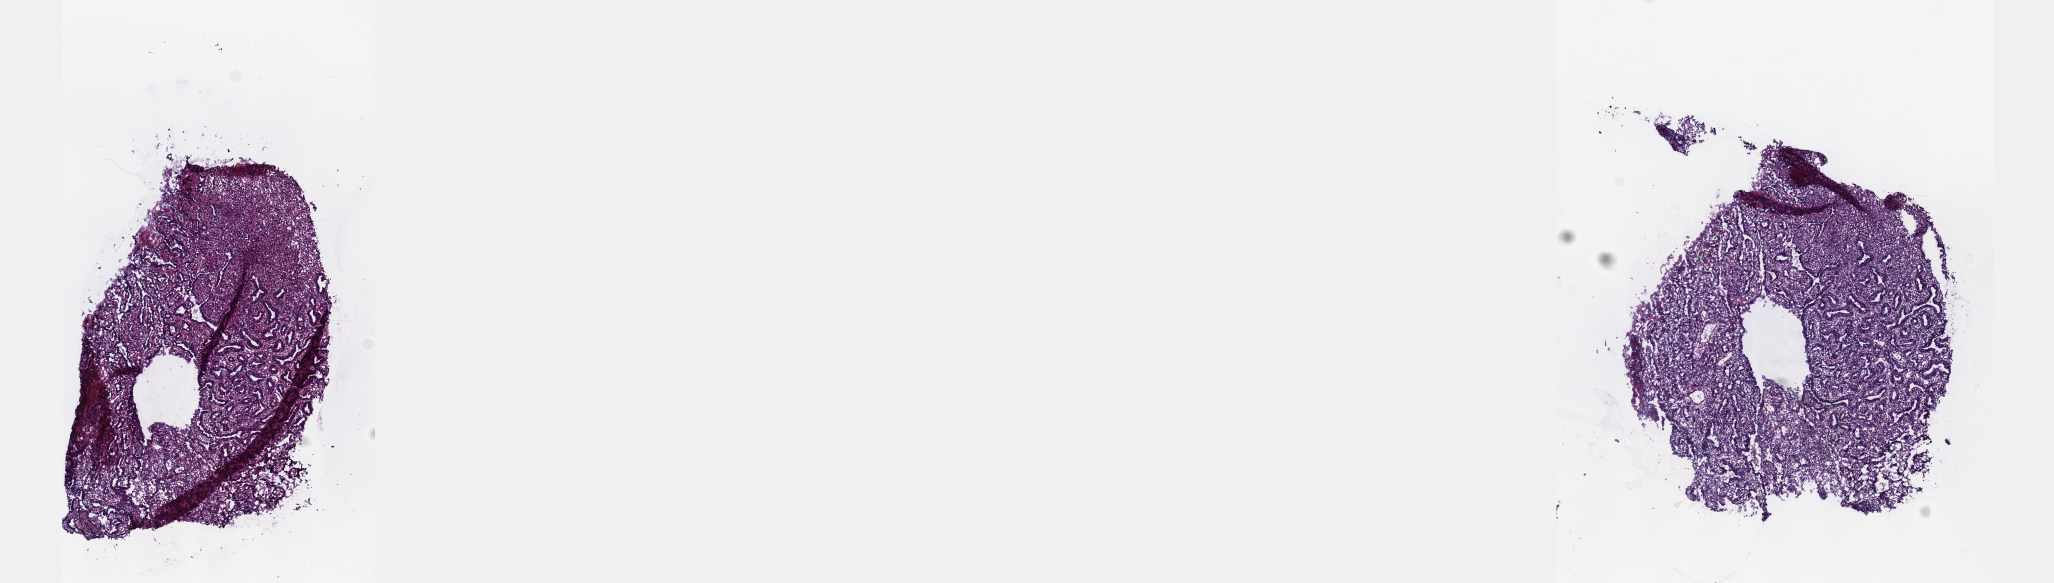
H&E-stained whole-slide image — low-resolution overview of the scanned area, about 16.6 x 4.7 mm (from a 40x scan). Frozen section from the top of the tissue portion. Stomach, primary tumour sample. Patient: male, age at initial diagnosis 63 years. Histologic grade: GX (grade cannot be assessed). Composition of this section per pathologist review: tumour cells 70%, tumour nuclei 70%, normal cells 0%, stromal cells 20%, necrosis 10%. Inflammatory infiltration, as recorded: lymphocyte infiltration 40%, monocyte infiltration 20%, neutrophil infiltration 20%.
Pathologic diagnosis: Tubular adenocarcinoma (body of stomach). AJCC pathologic stage: IIIB (7th edition). TNM: T4b N1 M0.